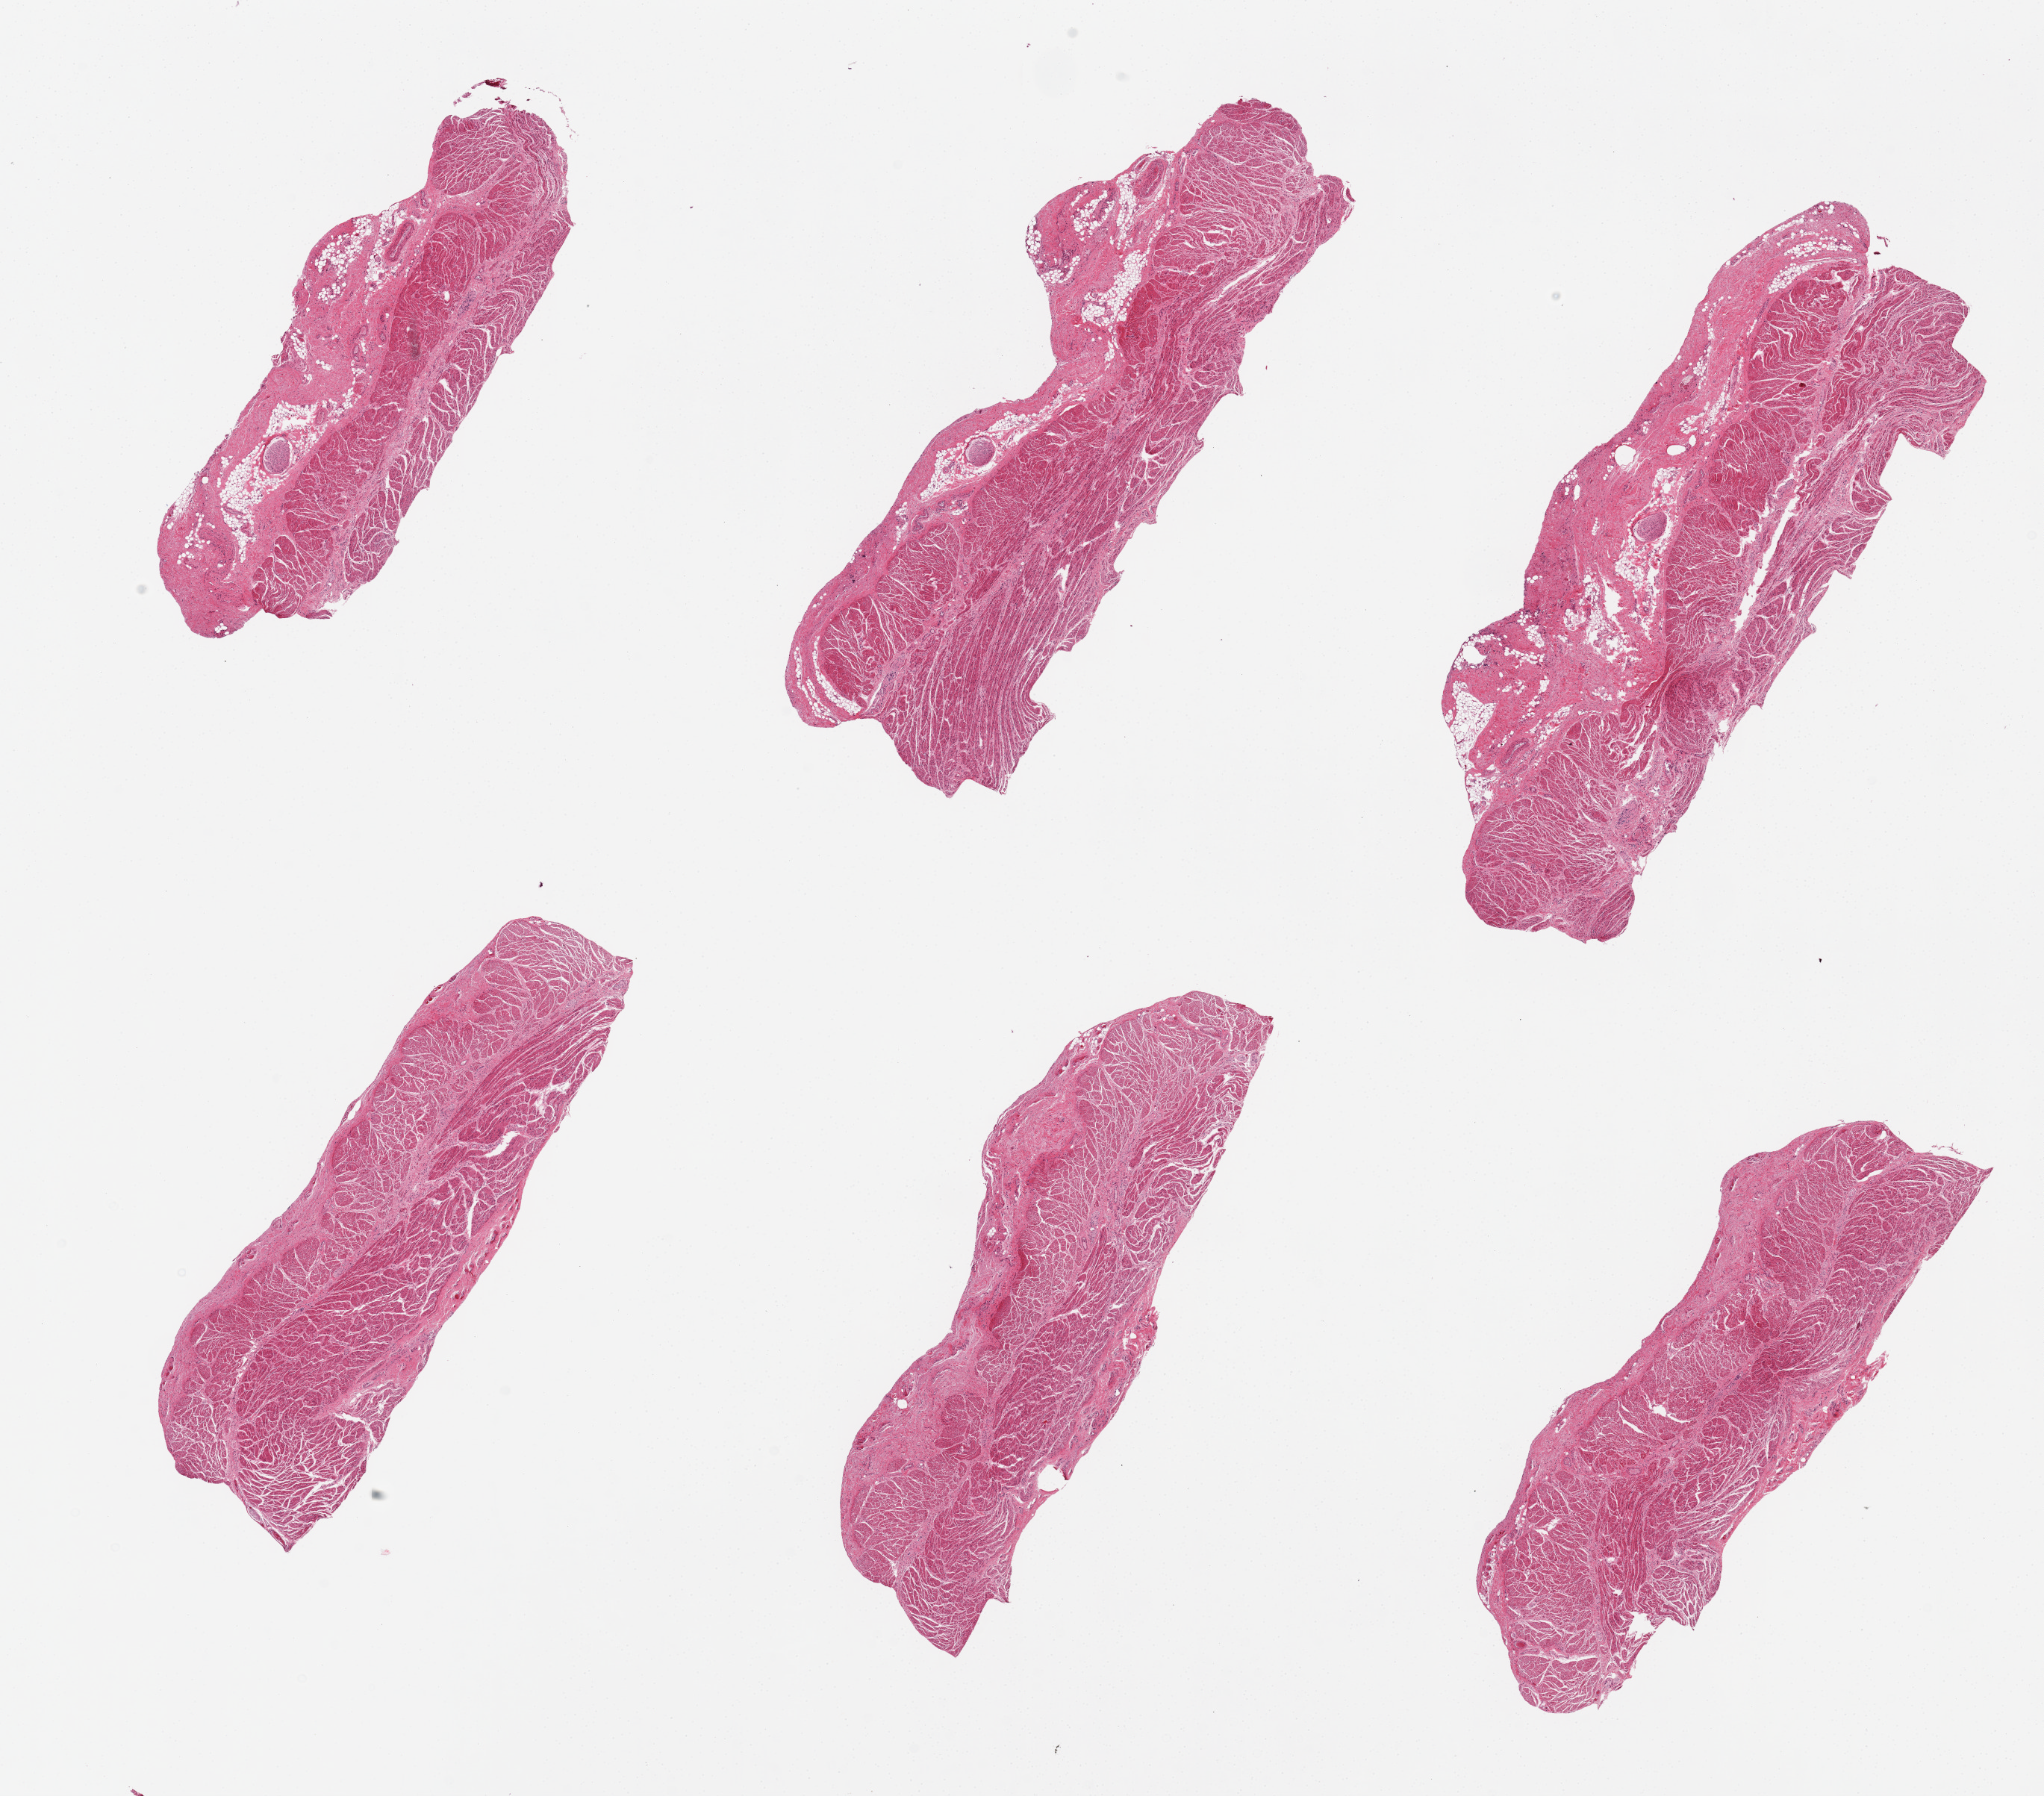
Whole-slide image, haematoxylin and eosin stain — shown as a low-resolution overview of the whole scanned area (about 21.7 x 19.0 mm, acquisition: 20x scan); PAXgene-fixed, paraffin-embedded tissue; section of gastroesophageal junction (target tissue); tissue donor sample. Donor: female.
Pathologist's review note for this sample: 6 pieces, all muscularis, excellent specimens.